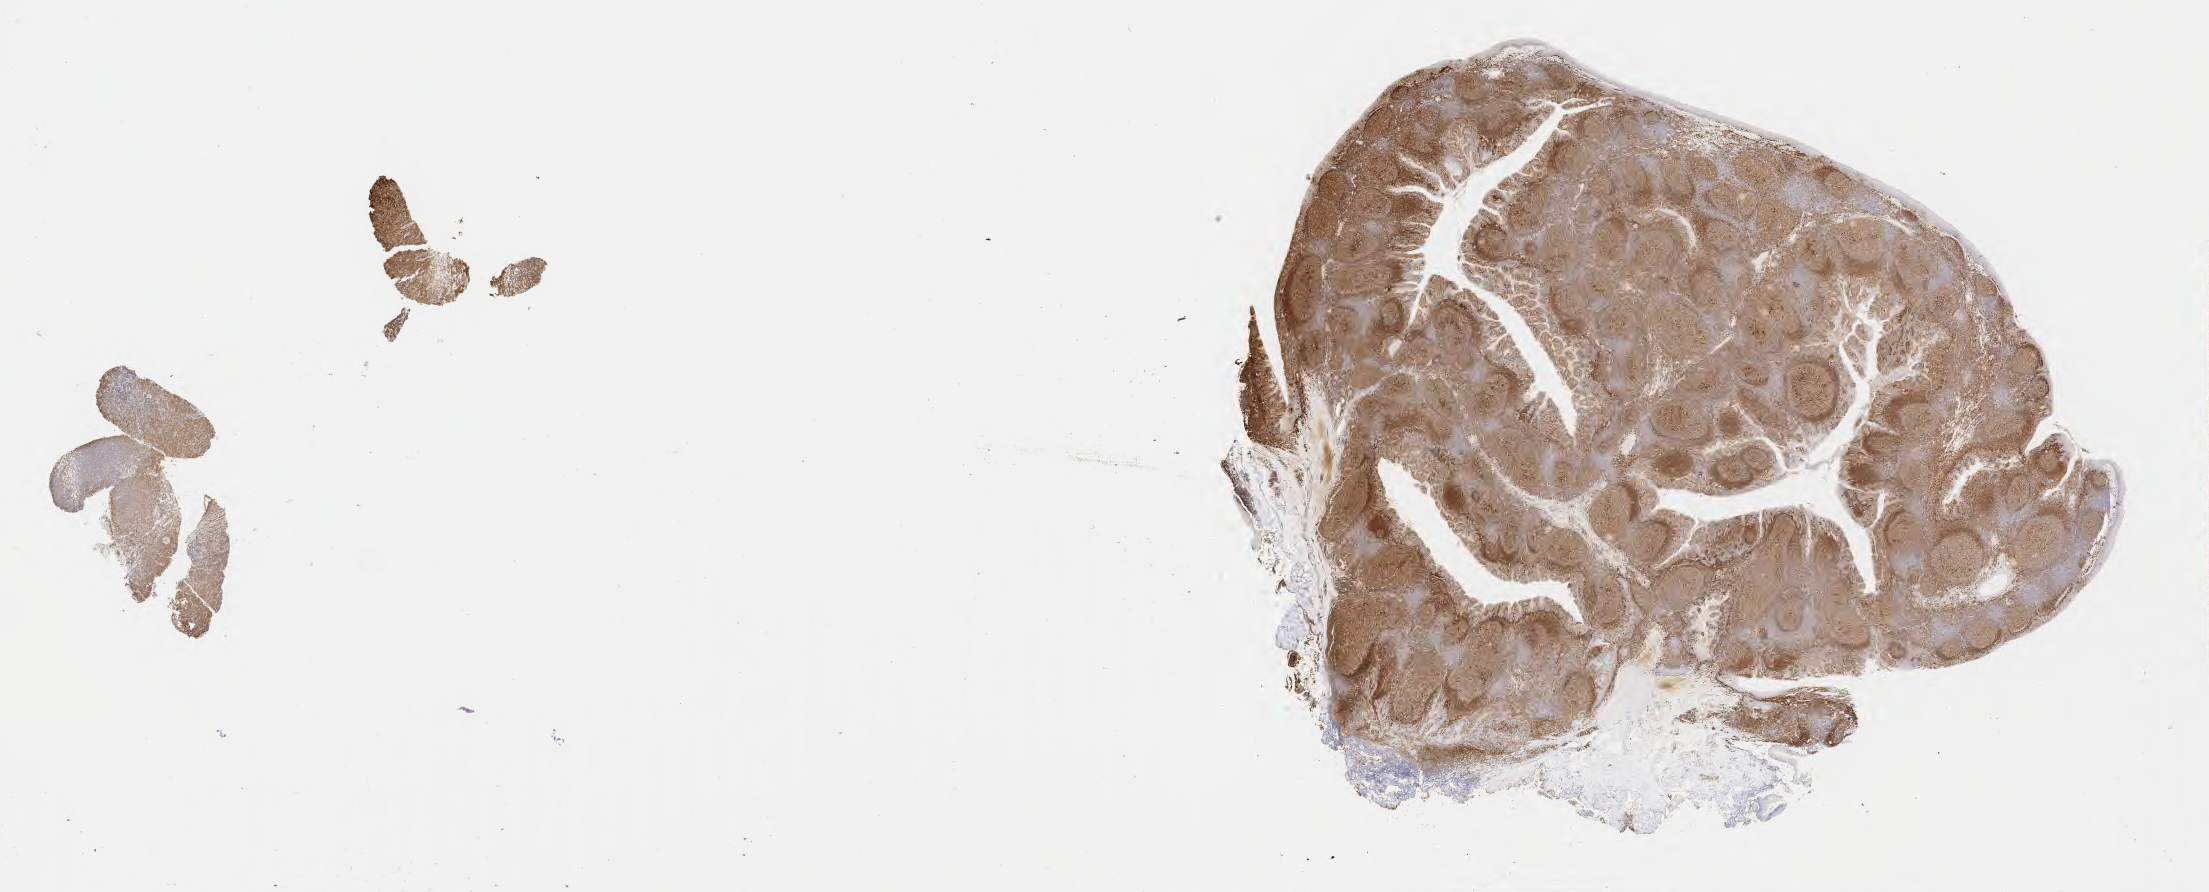
Immunohistochemistry (IHC) whole-slide image stained for CD79a, a low-resolution overview of the entire scanned area, about 35.7 x 14.4 mm; specimen: tumor tissue; anatomic site: lymph node. Male patient, age 54 years.
• histologic diagnosis: Diffuse large B-cell lymphoma, NOS